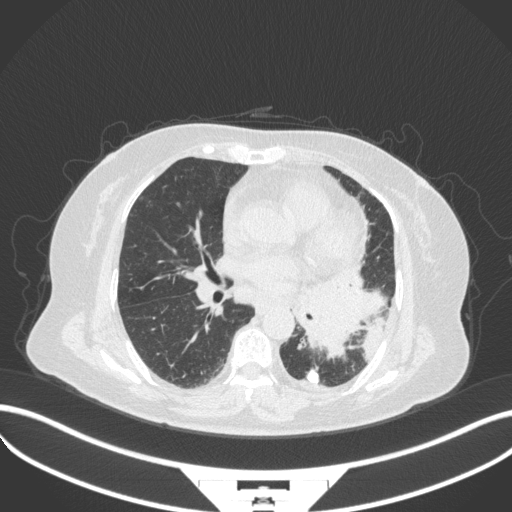
Chest CT, one axial slice; position 170 of 328 along the scan axis; 120 kVp; lung window (W 1500 / L -600 HU); 1 mm slice thickness; 512 × 512 image matrix, field of view 400 × 400 mm. Female patient, age 69 years. Case-level facts recorded for this patient, not image findings: clinical TNM (as recorded): T2b N3 M1.
Annotated regions visible in this slice (rectangle marked by the reading radiologist):
- lung tumour (recorded histology: adenocarcinoma): bounding box [x1, y1, x2, y2] px = [291, 282, 391, 361]